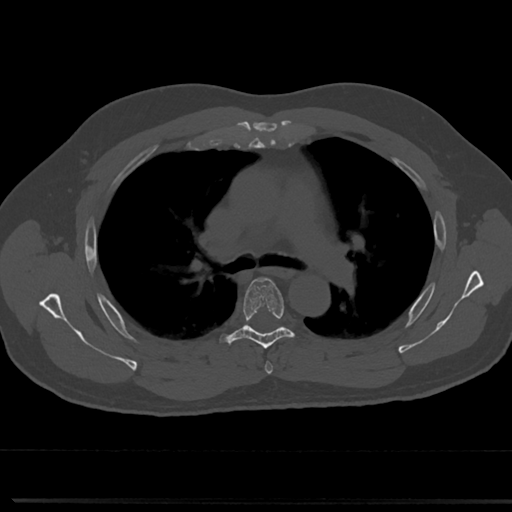
CT including the spine, one axial slice; slice 502 of 817 in the series (ordered by position); reconstruction kernel Br40s/3; bone window (W 1800 / L 400 HU); 0.5 mm slice thickness; 512 × 512 image matrix. Patient: male, 61 years. Case-level facts recorded for this patient, not image findings: primary cancer: prostate.
Annotated regions visible in this slice (semi-automatic segmentation, software-assisted and operator-edited):
- T4 vertebra: bounding box <264,350,273,374> (left, top, right, bottom; pixels)
- T5 vertebra: <218,276,309,352>